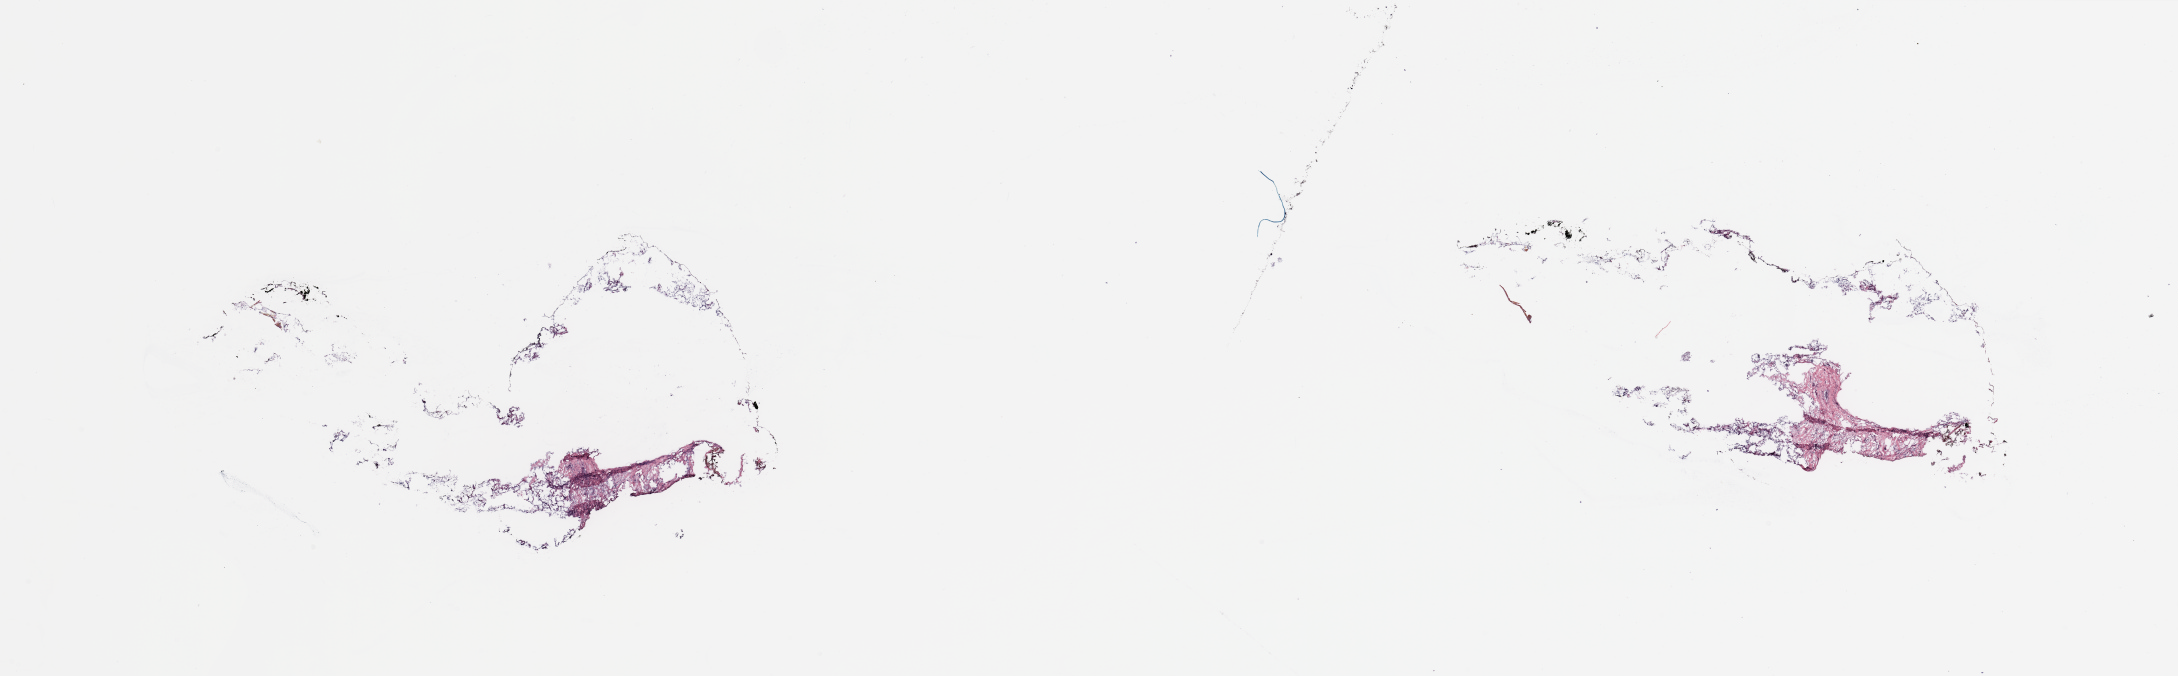
Digitized H&E-stained tissue section (whole slide) — shown as a low-resolution overview of the whole scanned area (about 34.5 x 10.7 mm, slide scanned at 20x). Tumour tissue sample, breast. Female, 61 y/o.
AJCC pathologic stage: IIA. Histologic diagnosis: Infiltrating lobular carcinoma, NOS.